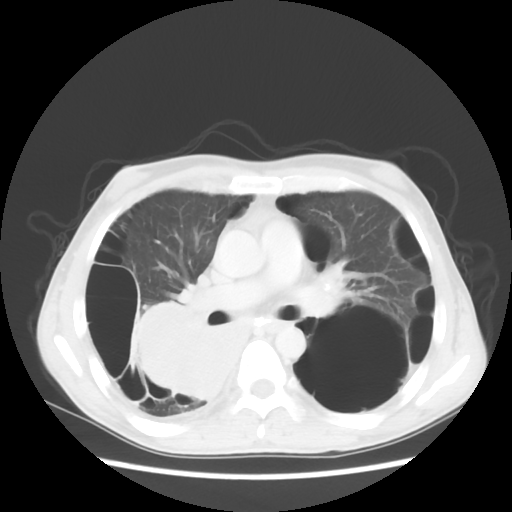
Chest CT, one axial slice; reconstruction kernel STANDARD; lung window (W 1500 / L -600 HU); 5 mm slice thickness; 512 × 512 image matrix, field of view 351 × 351 mm. Male patient, age 41 years. From the clinical record (not read from this slice): clinical TNM (as recorded): T4 N0 M1a; histopathological grade: G3.
Outlined on this slice (rectangle marked by the reading radiologist):
- lung tumour (recorded histology: large cell carcinoma): box from (x=121, y=303) to (x=244, y=416) px